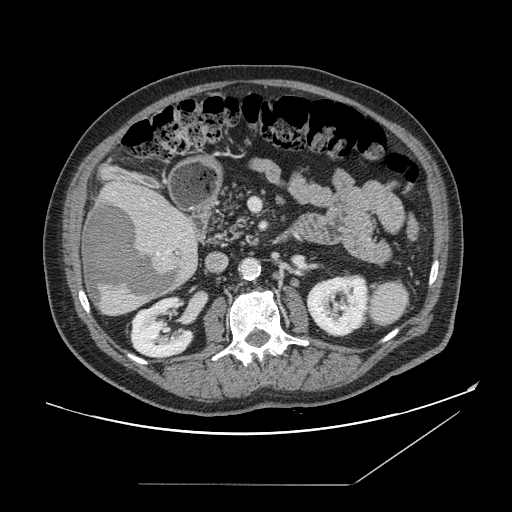
Contrast-enhanced abdominal CT, one axial slice; position 67 of 166 along the scan axis; 120 kVp; intravenous contrast given; soft-tissue window (W 400 / L 40 HU); 2.5 mm slice thickness; 512 × 512 image matrix. Male patient, age 80 years. From the clinical record (not read from this slice): diagnosis: colorectal cancer liver metastases, imaged before liver resection.
Annotated regions visible in this slice (manually delineated by an expert):
- liver: bounding box <81,181,199,316> (left, top, right, bottom; pixels)
- planned liver remnant (the part of the liver to remain after resection): <113,181,178,213>
- liver metastasis: <84,202,181,308>